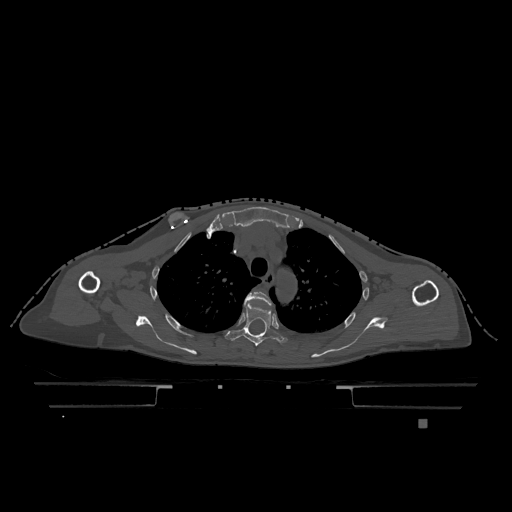
CT including the spine, one axial slice; slice 889 of 1317 in the series (ordered by position); bone window (W 1800 / L 400 HU); 512 × 512 image matrix, field of view 500 × 500 mm. Patient: female, 74 years. Case-level facts recorded for this patient, not image findings: primary cancer: lung; vertebrae with lytic lesions (as recorded): T1, T4, T5, T6, L4, L5.
Structures marked on this image (semi-automatic segmentation, software-assisted and operator-edited):
- T3 vertebra: bounding box (x1, y1, x2, y2) in pixels: (244, 291, 271, 305)
- T4 vertebra: (224, 304, 288, 346)